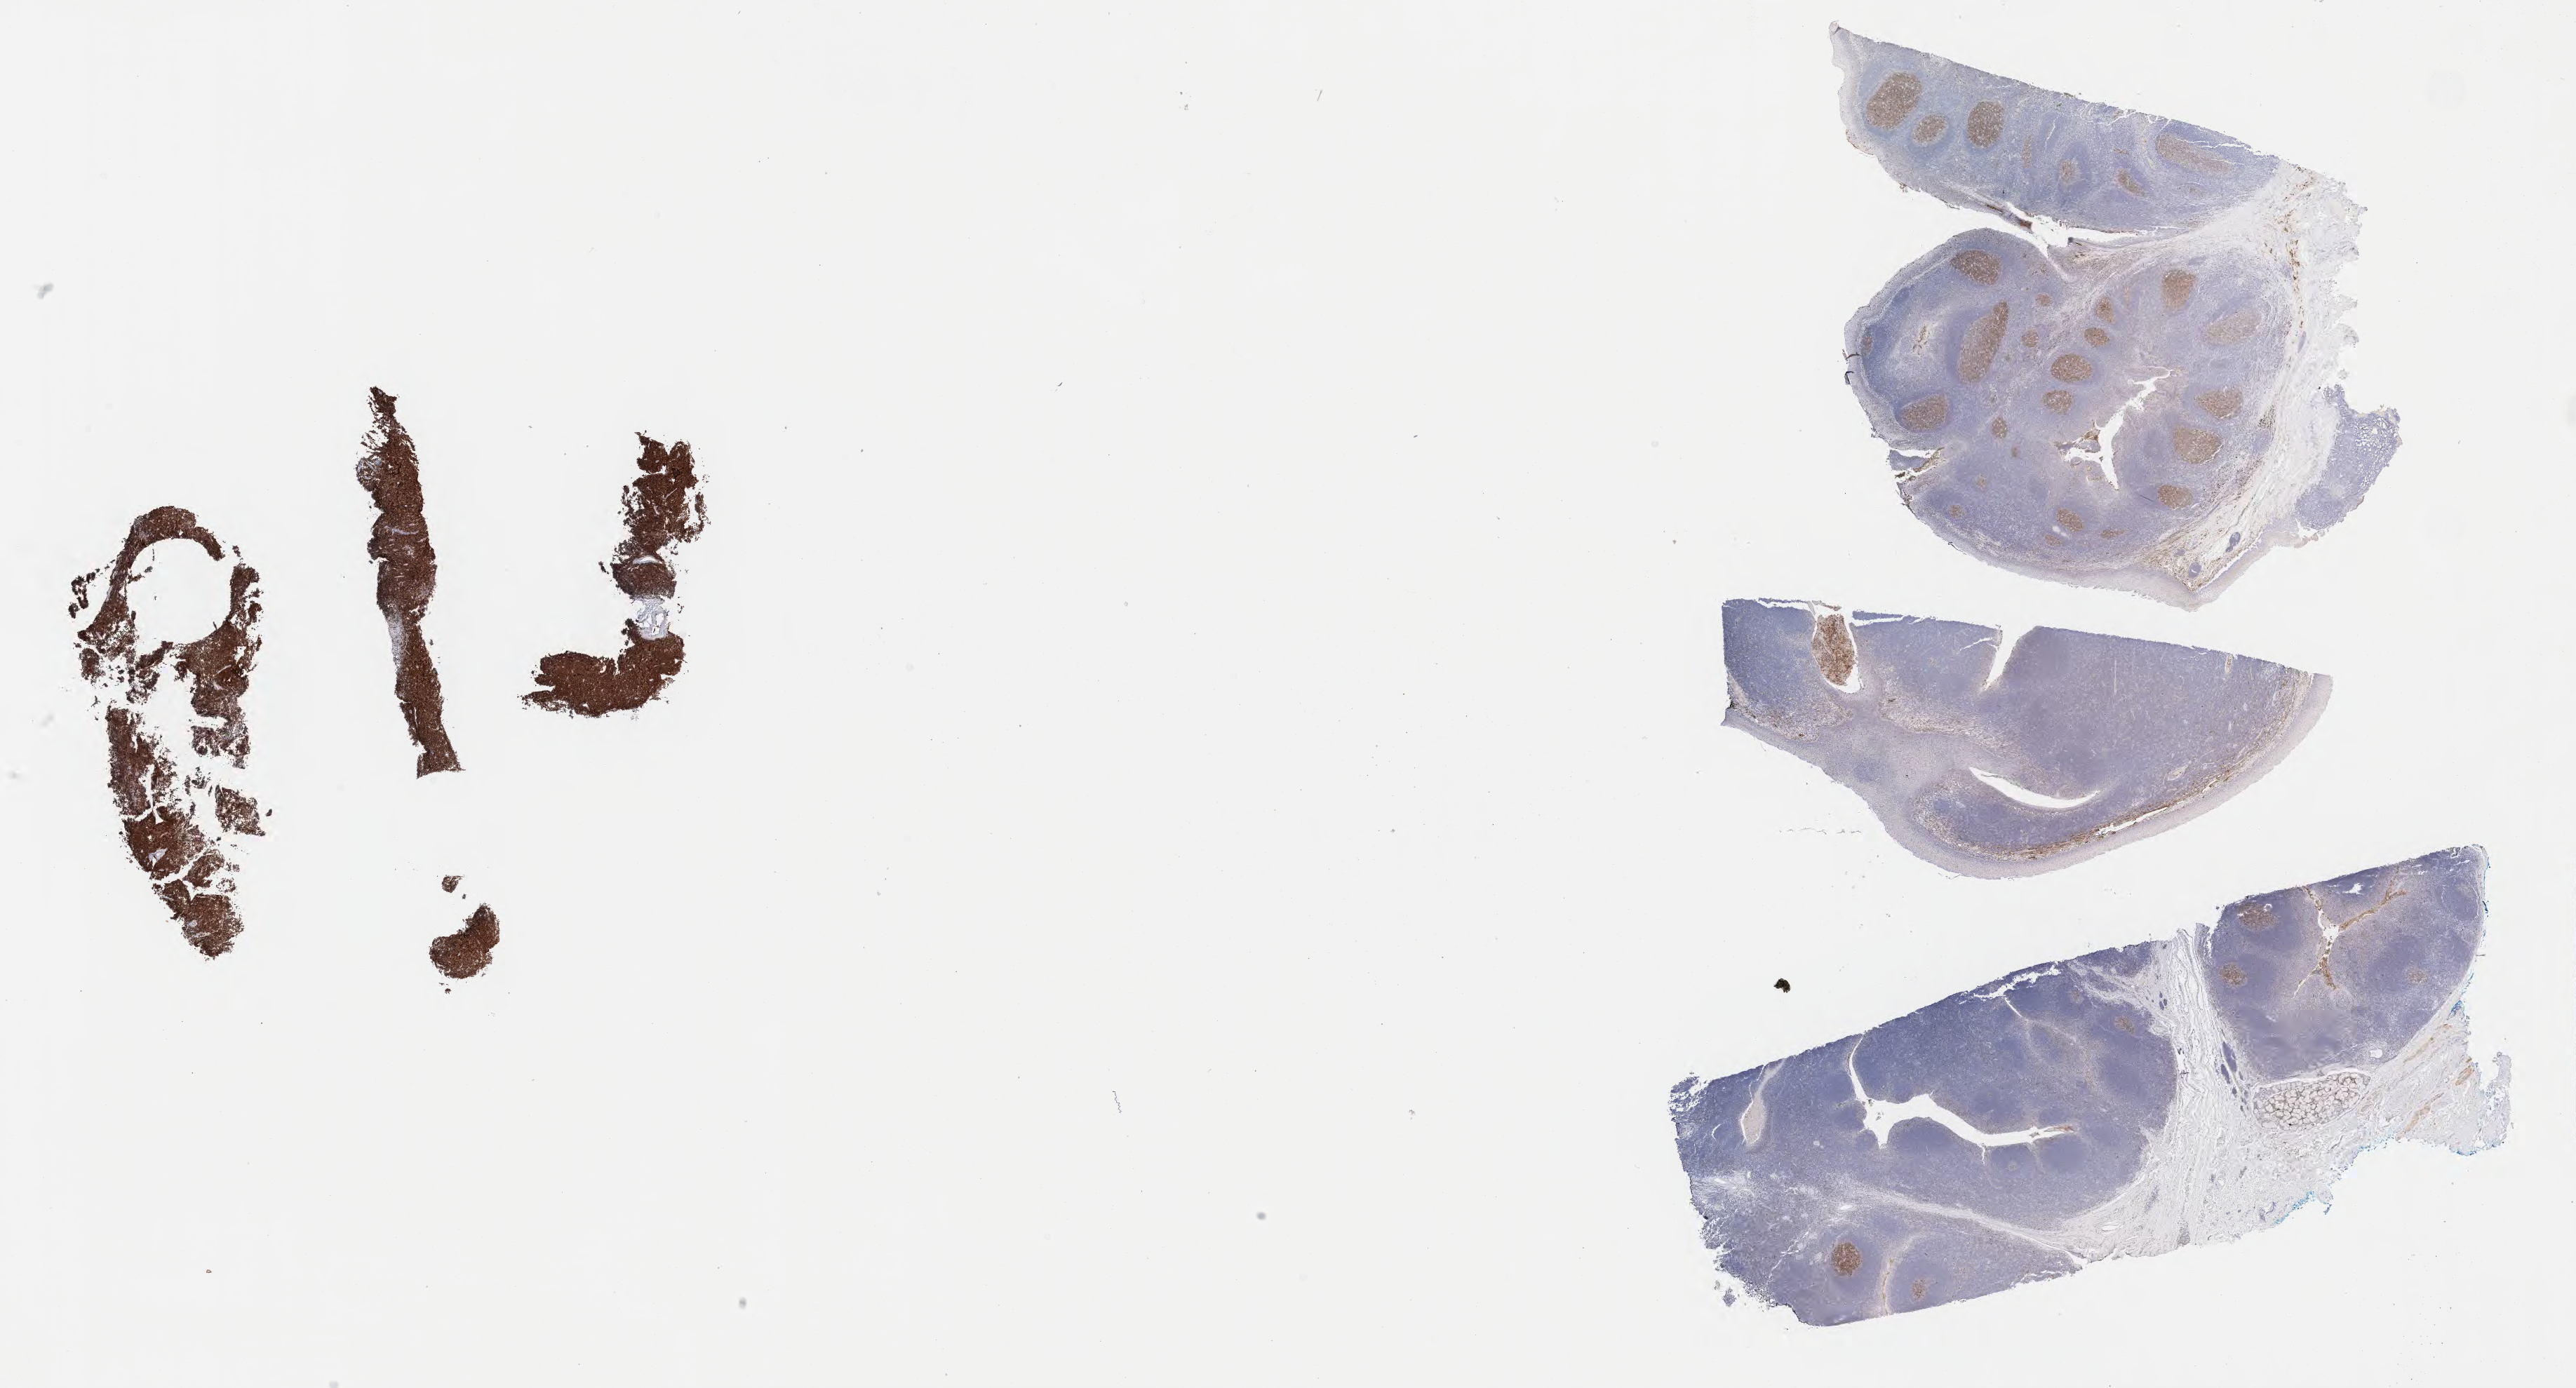
Whole-slide image, immunohistochemical stain for CD10, a low-resolution overview of the entire scanned area, about 29.7 x 16.0 mm. Specimen: tumor tissue. Anatomic site: spleen. Patient: male, age at initial diagnosis 8 years.
Histologic diagnosis: Burkitt lymphoma, NOS.